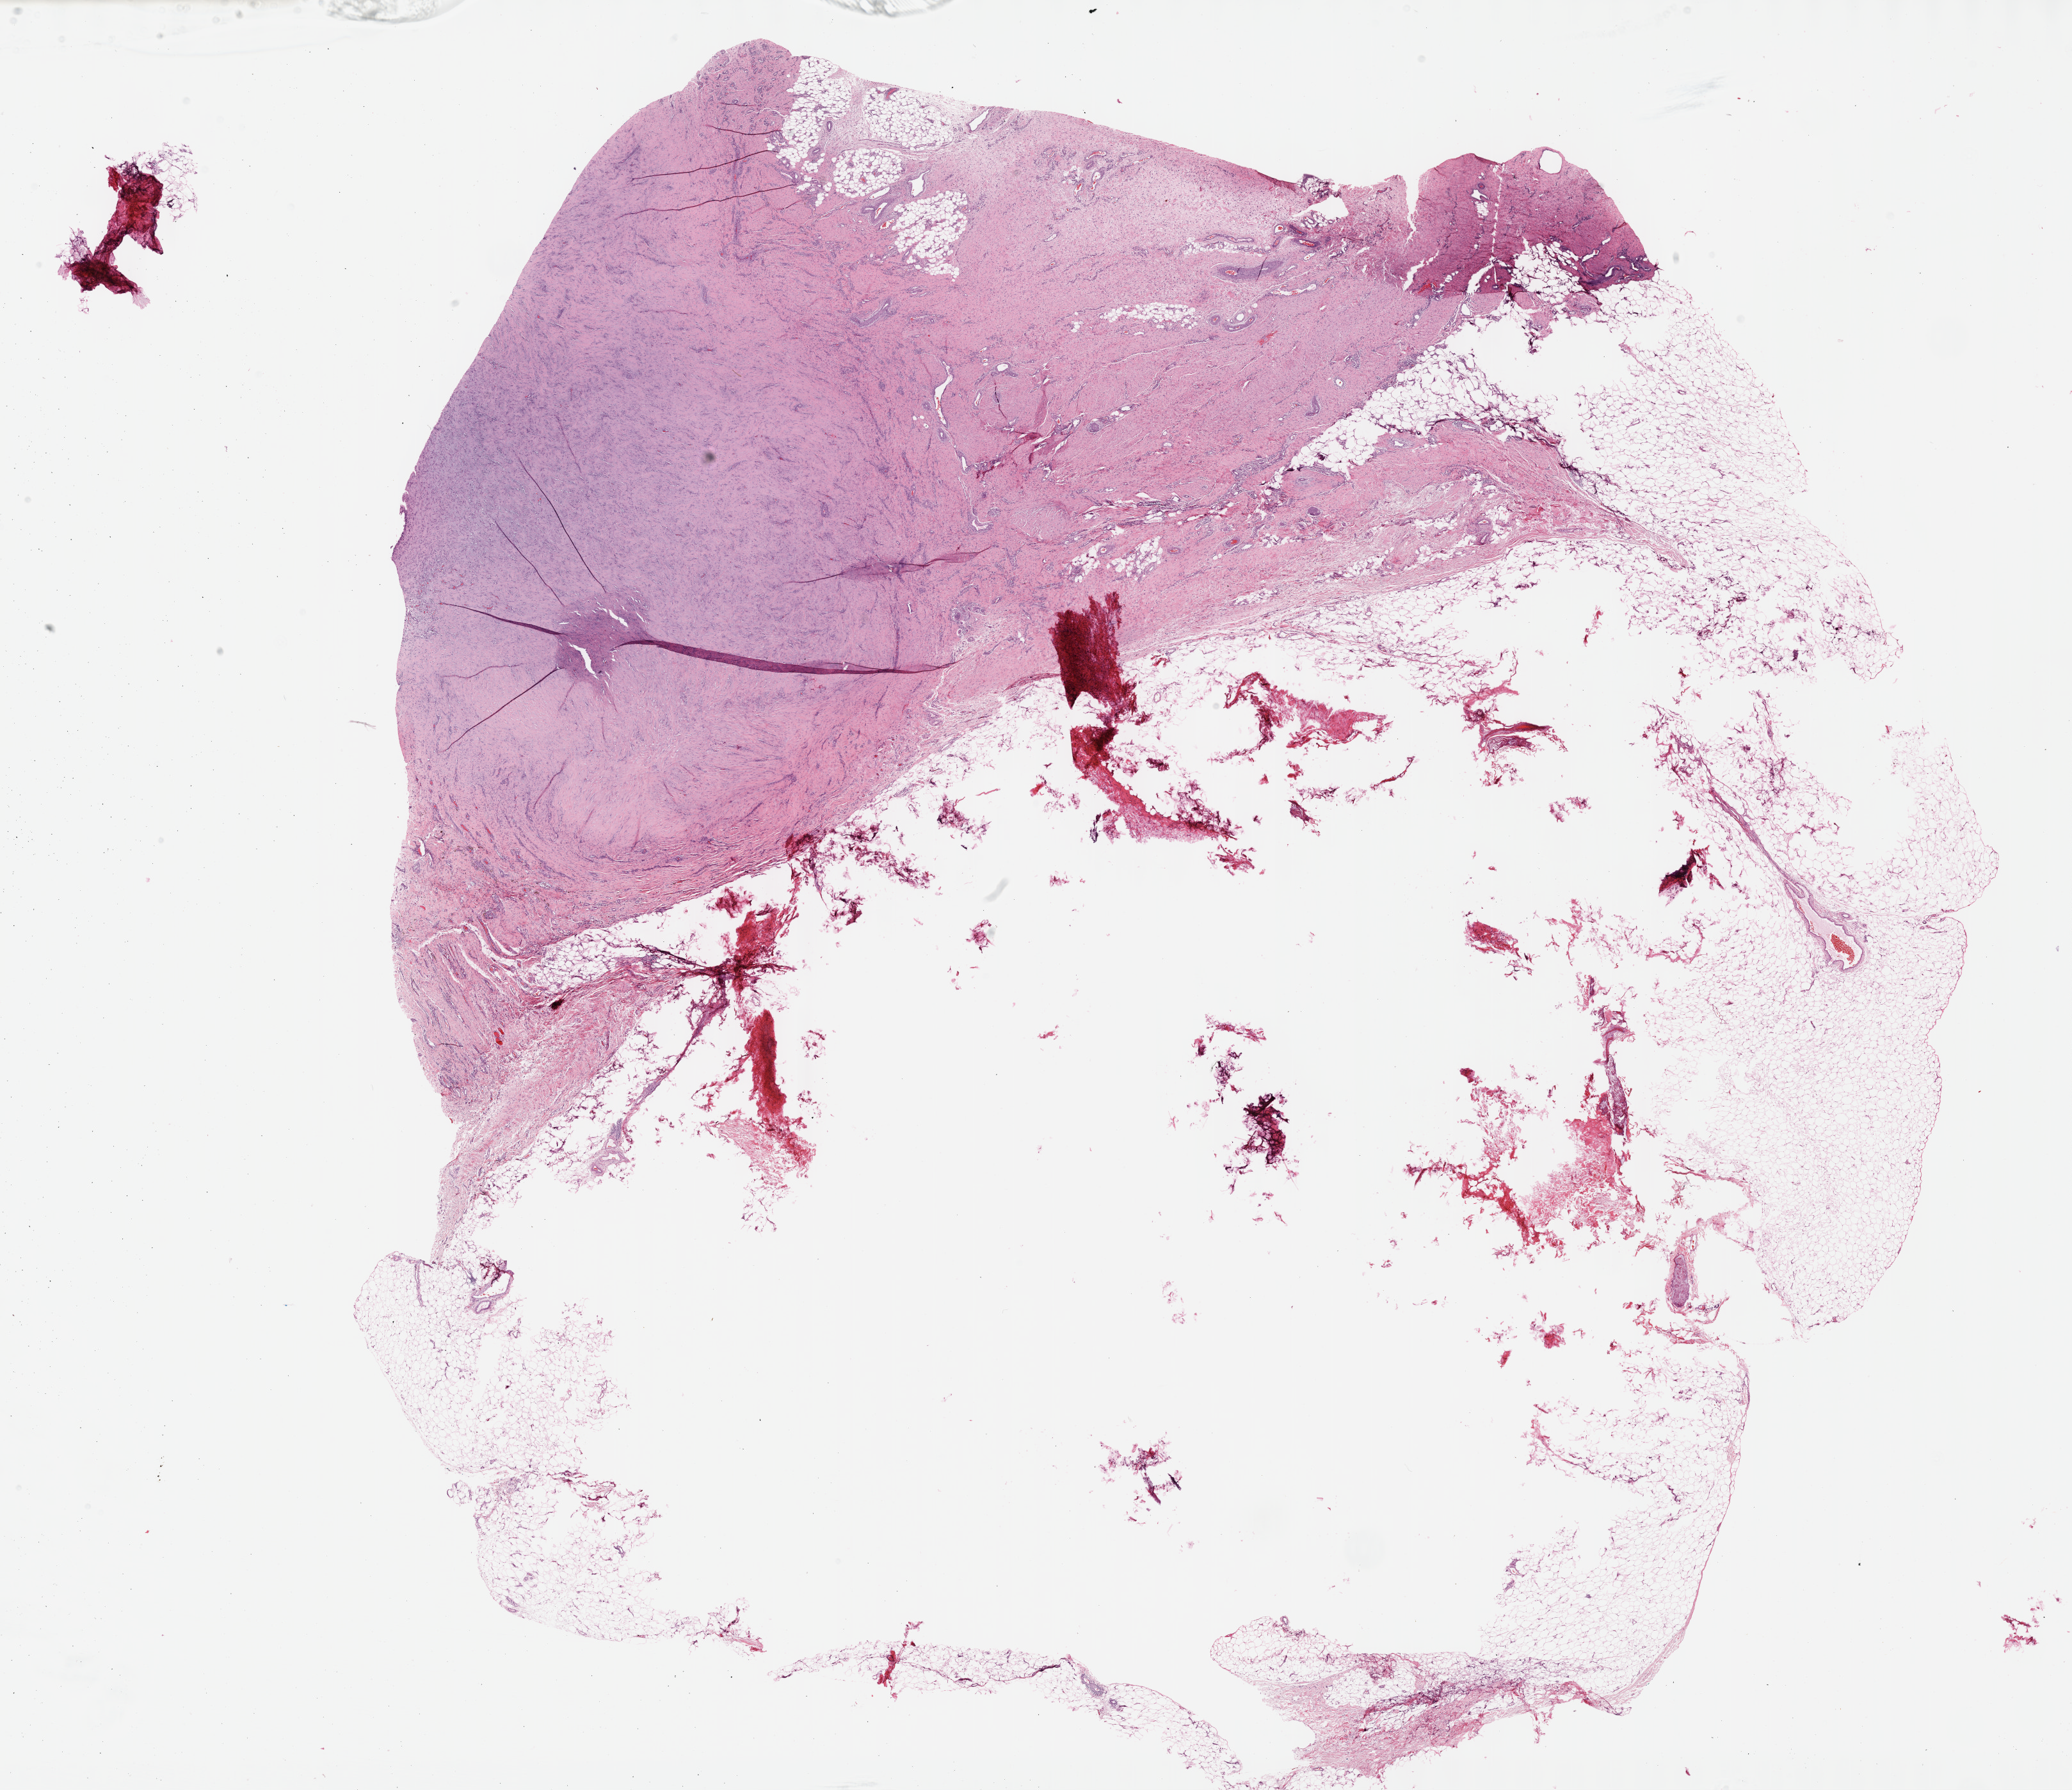
Whole-slide histology image, Hematoxylin and eosin (H&E) stained — a low-resolution overview of the entire scanned area, about 26.2 x 22.6 mm (from a 40x scan). Formalin-fixed paraffin-embedded (FFPE) diagnostic section. Sample: primary tumour, connective, subcutaneous and other soft tissues. Patient: male, age at initial diagnosis 35 years.
Histologic diagnosis: Fibromyxosarcoma (connective, subcutaneous and other soft tissues of lower limb and hip).